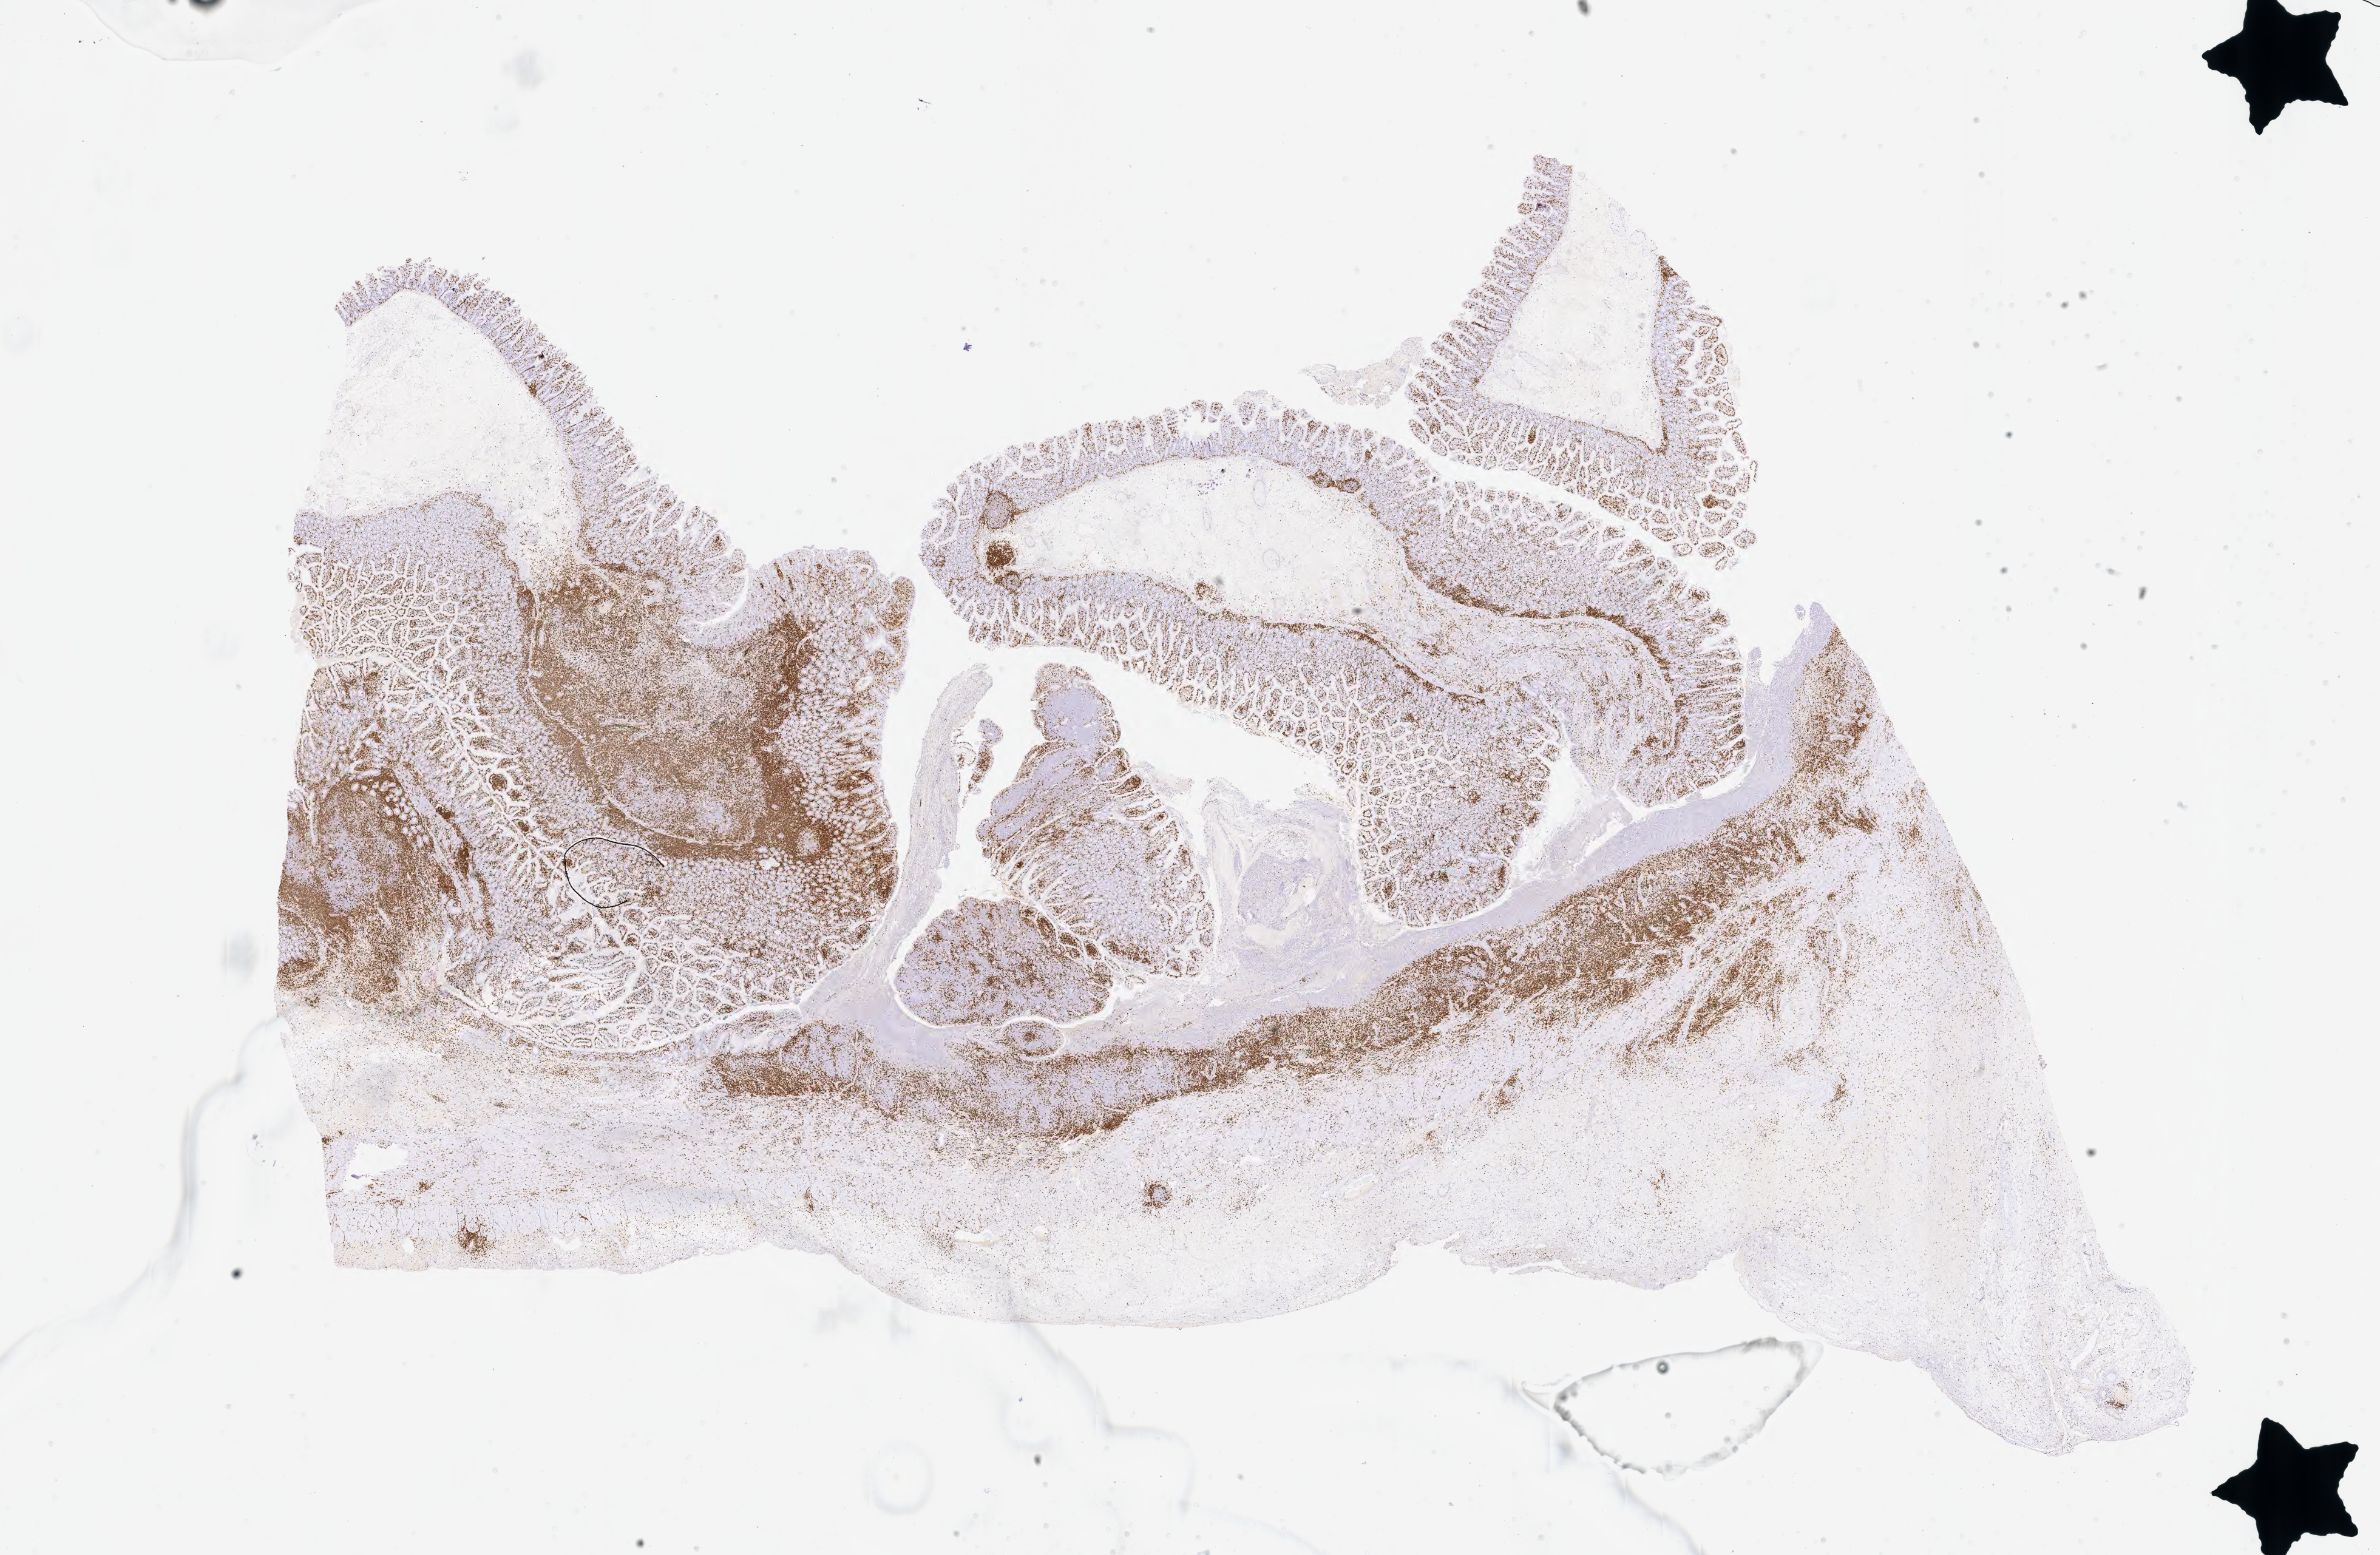
Whole-slide image, immunohistochemical stain for CD3 — low-resolution overview of the scanned area, about 31.7 x 20.7 mm; specimen: tumor tissue. Patient: female, aged 44.
Histologic diagnosis: Burkitt lymphoma, NOS.